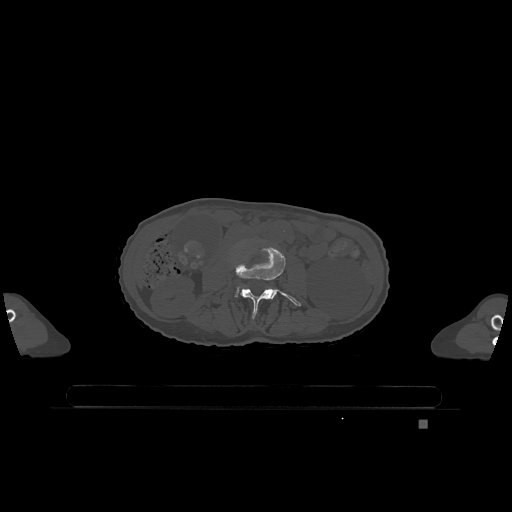
CT including the spine, one axial slice; slice 348 of 1317 in the series (ordered by position); bone window (W 1800 / L 400 HU); 0.5 mm slice thickness; 512 × 512 image matrix. Patient: female, 74 years. From the clinical record (not read from this slice): primary cancer: lung.
Outlined on this slice (semi-automatic segmentation, software-assisted and operator-edited):
- L3 vertebra: bounding box <235,247,301,318> (left, top, right, bottom; pixels)
- L4 vertebra: <235,289,238,297>